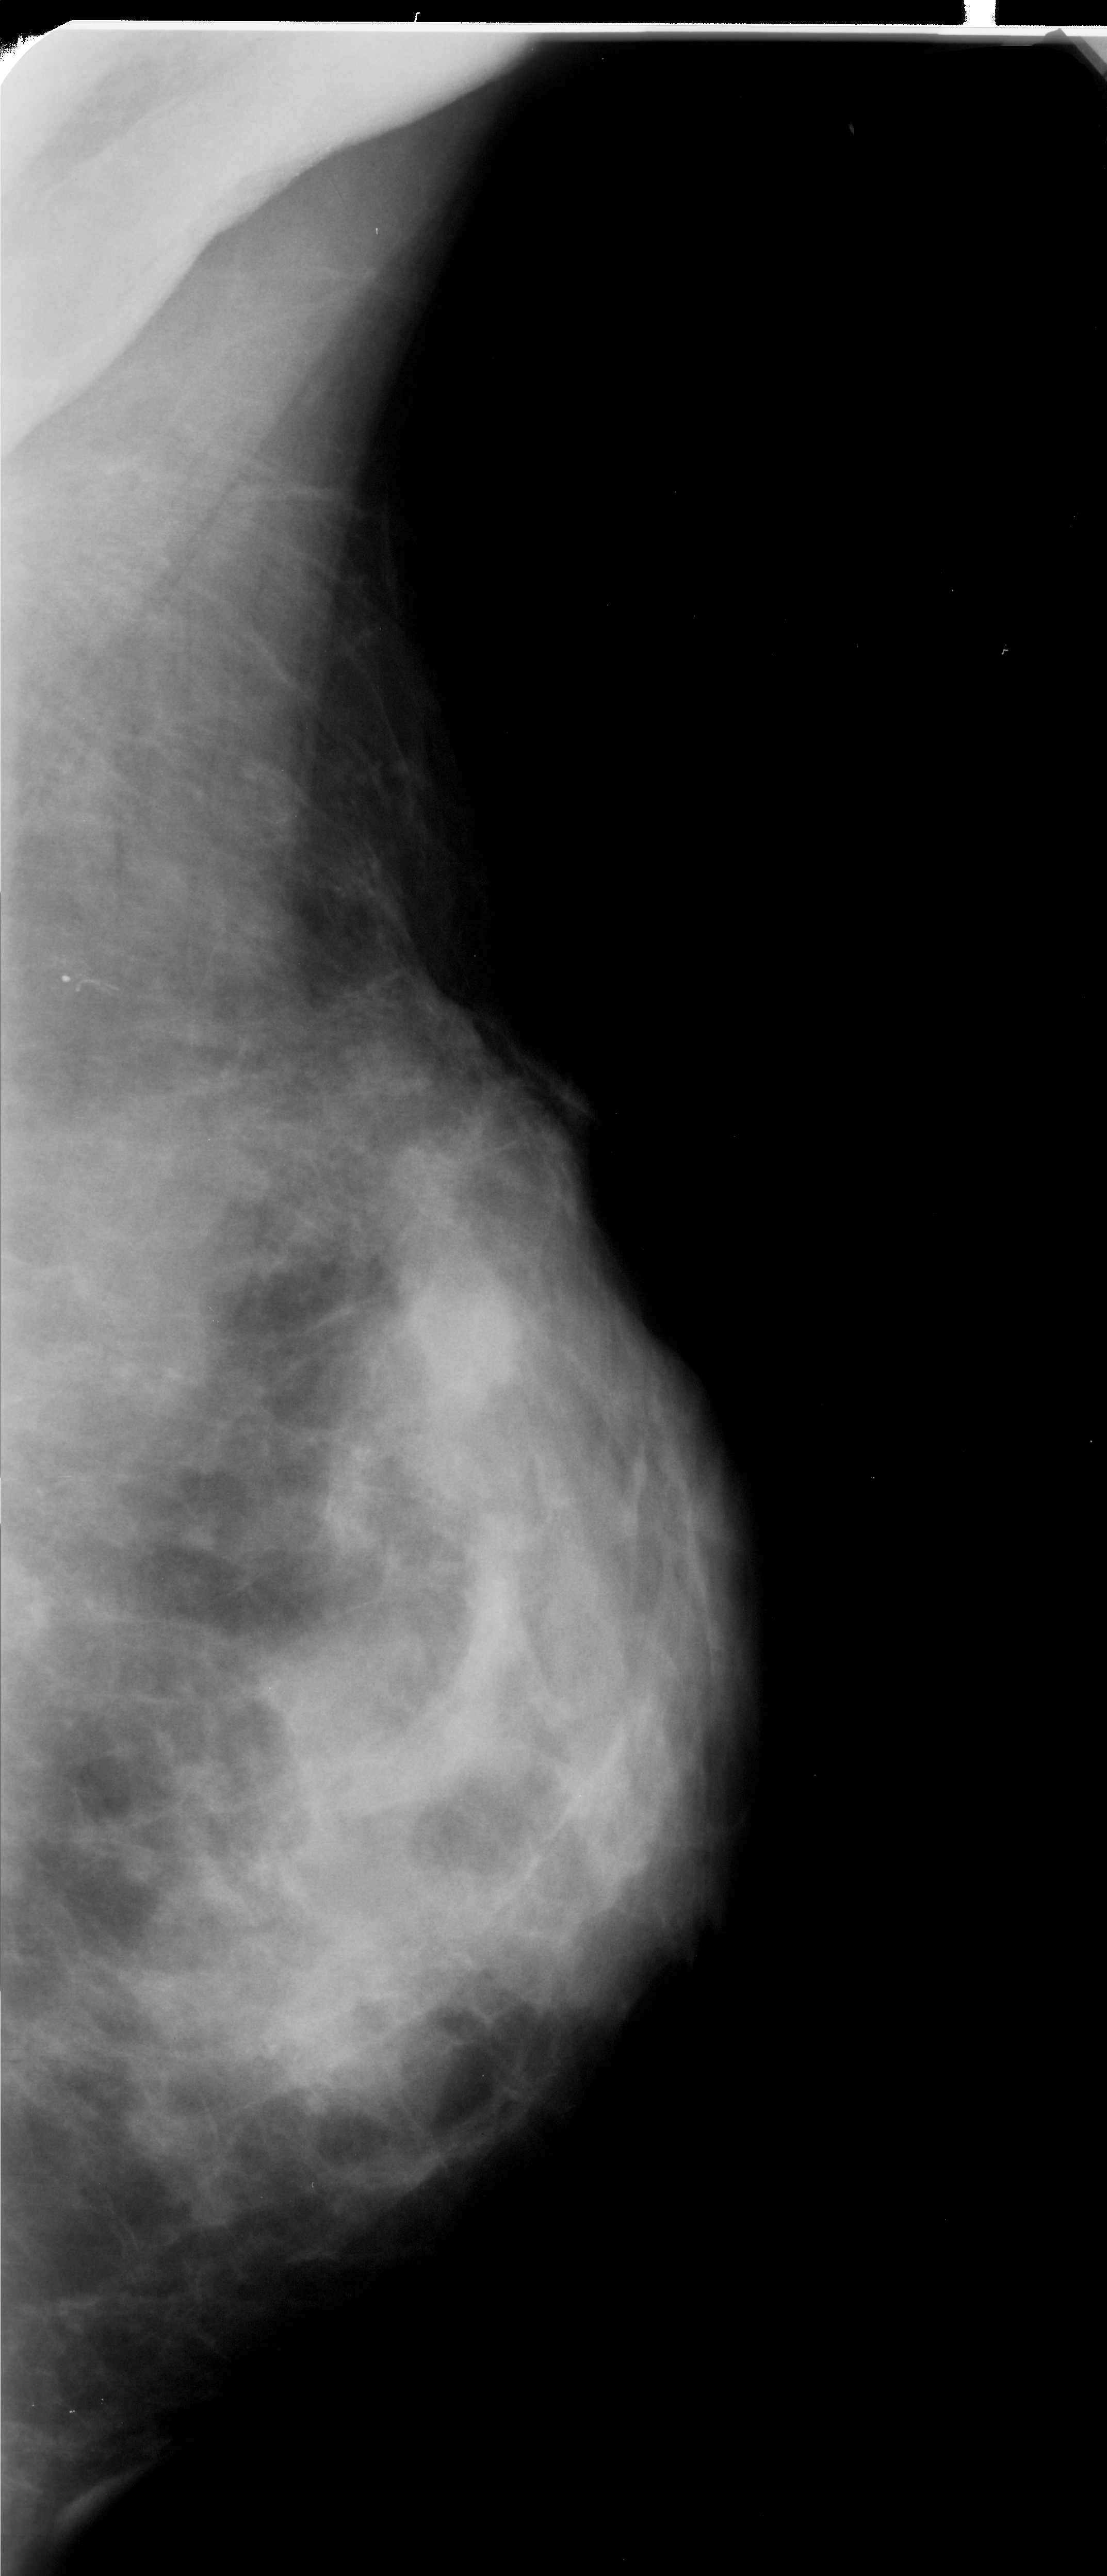
Digitized screen-film mammogram; right breast; mediolateral oblique (MLO) view; 1107 × 2576 image matrix.
Marked abnormalities (boxes around the expert regions of interest):
- calcifications, morphology fine linear branching, distribution linear; BI-RADS assessment category 4; pathology (as recorded): malignant: box from (x=39, y=954) to (x=152, y=1023) px